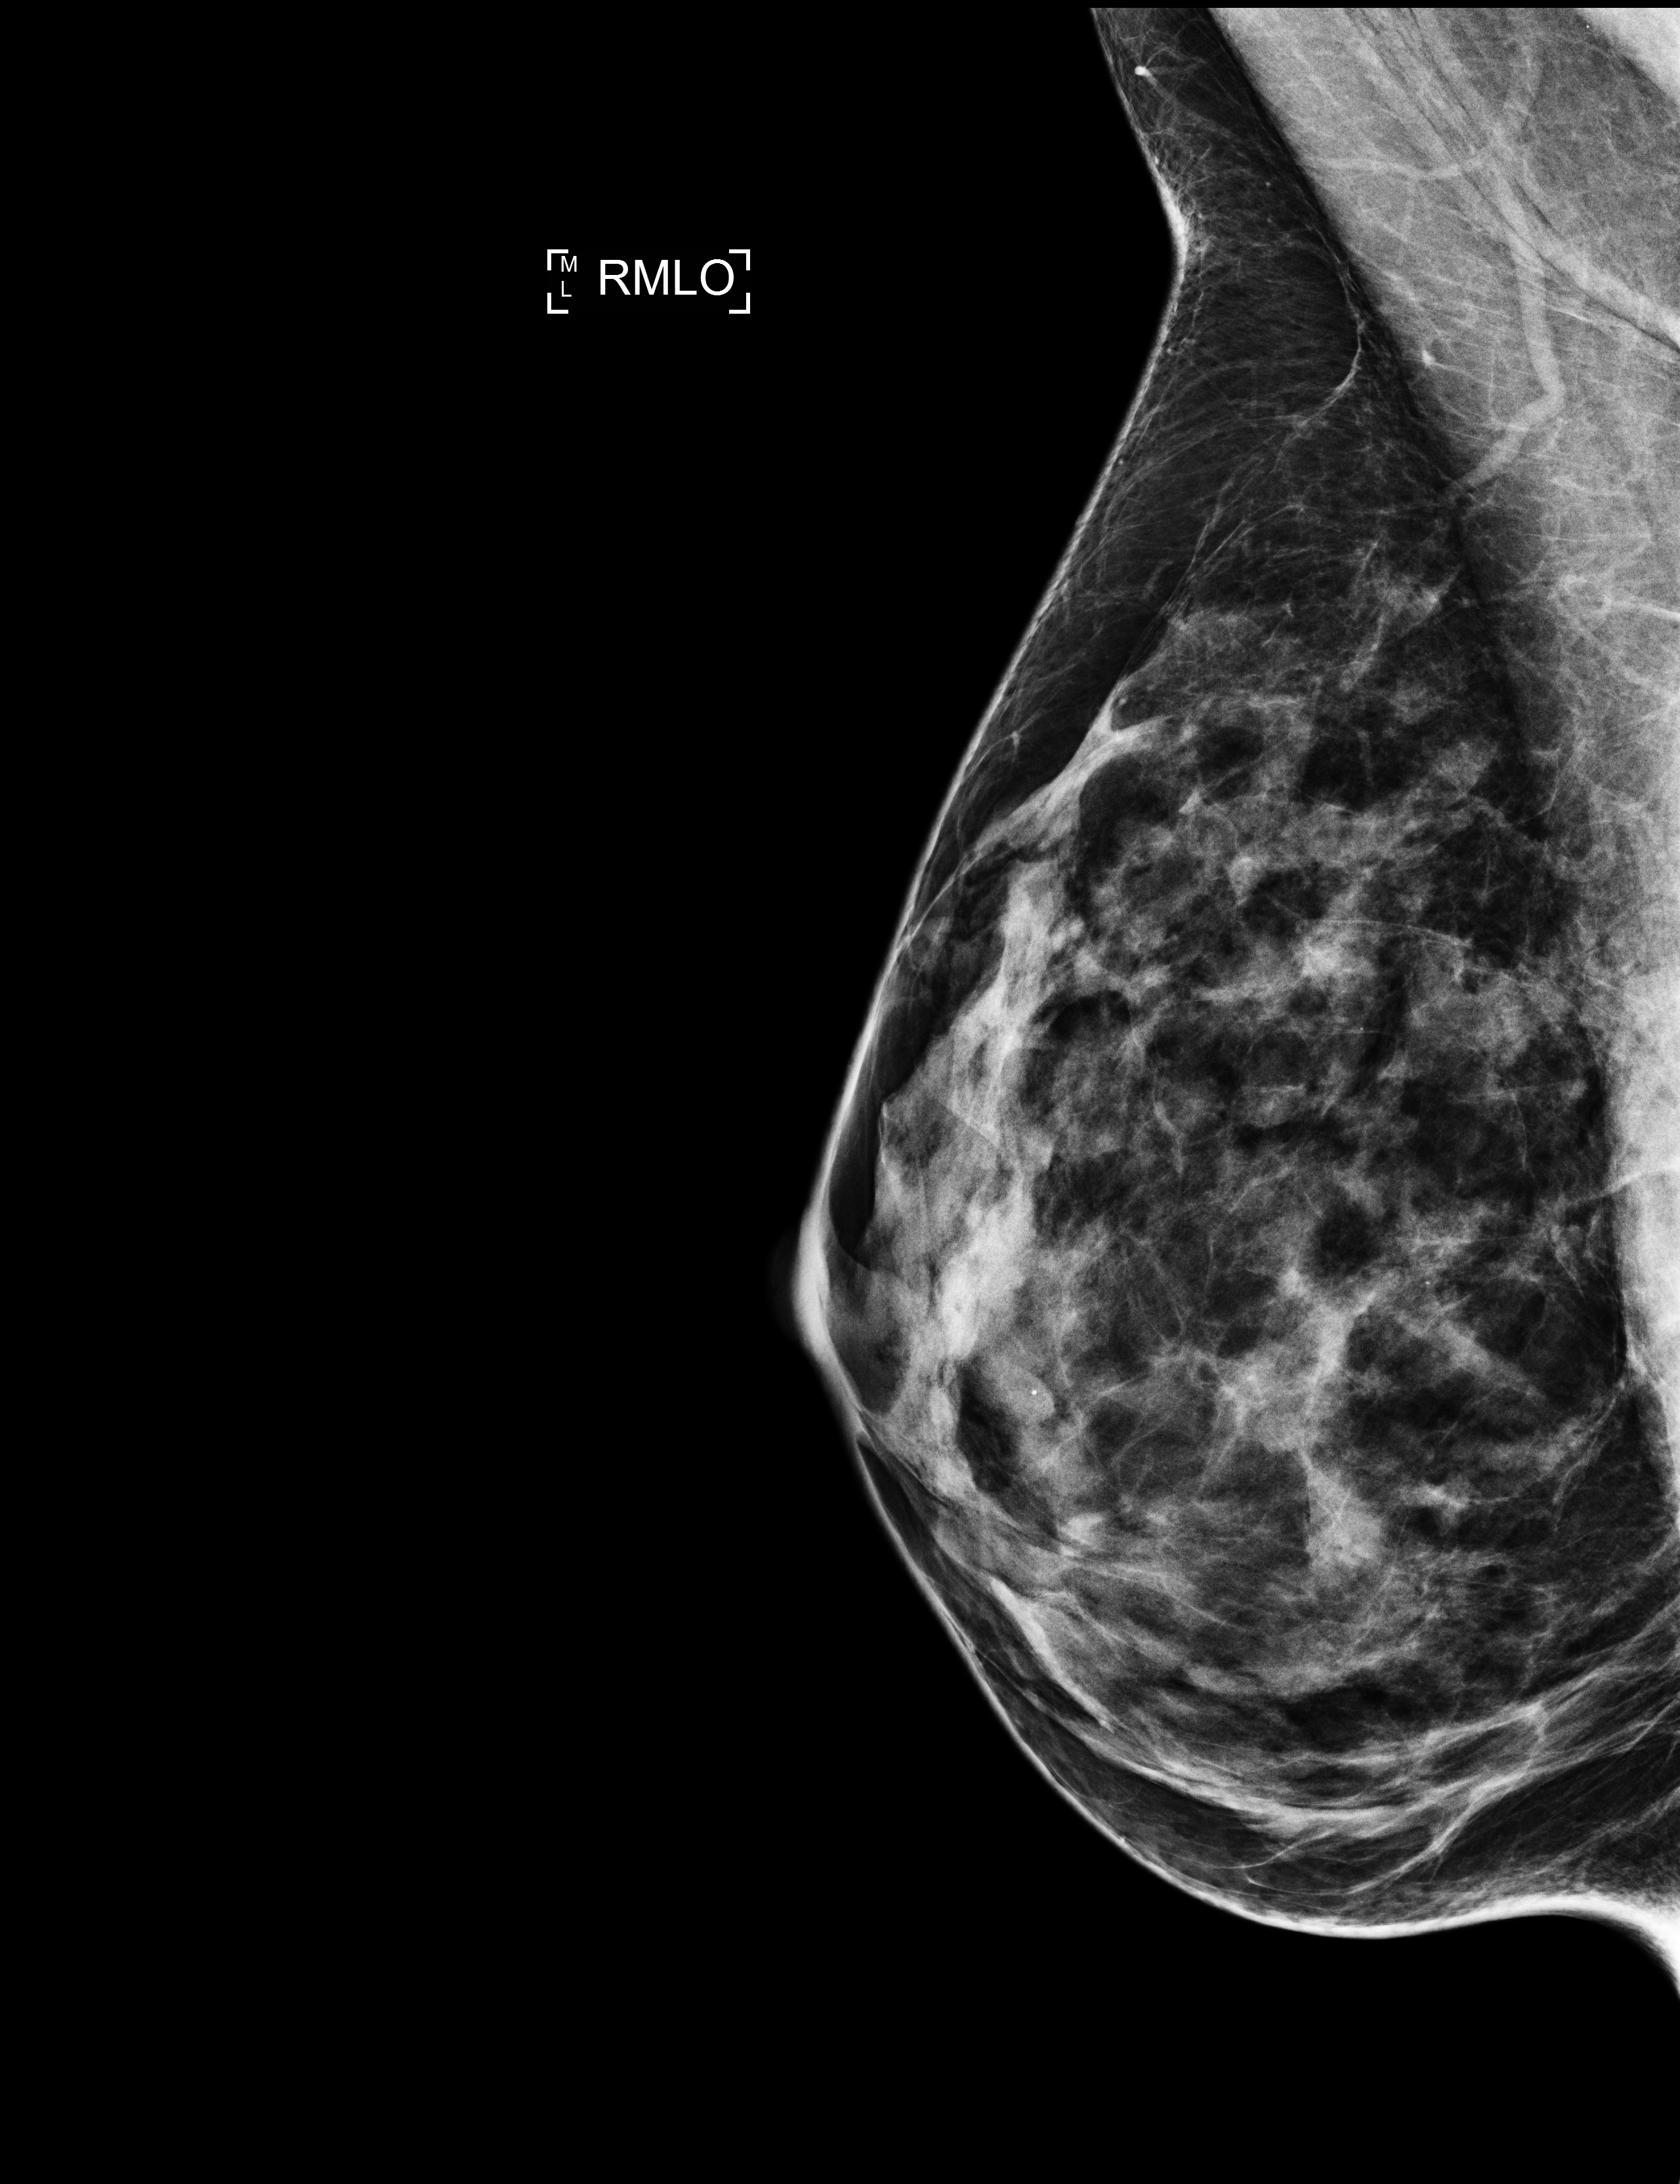
Annual screening mammography examination. Female patient, age 53 years.
Image type: full-field digital mammogram. Breast: right. Projection: medio-lateral oblique projection.